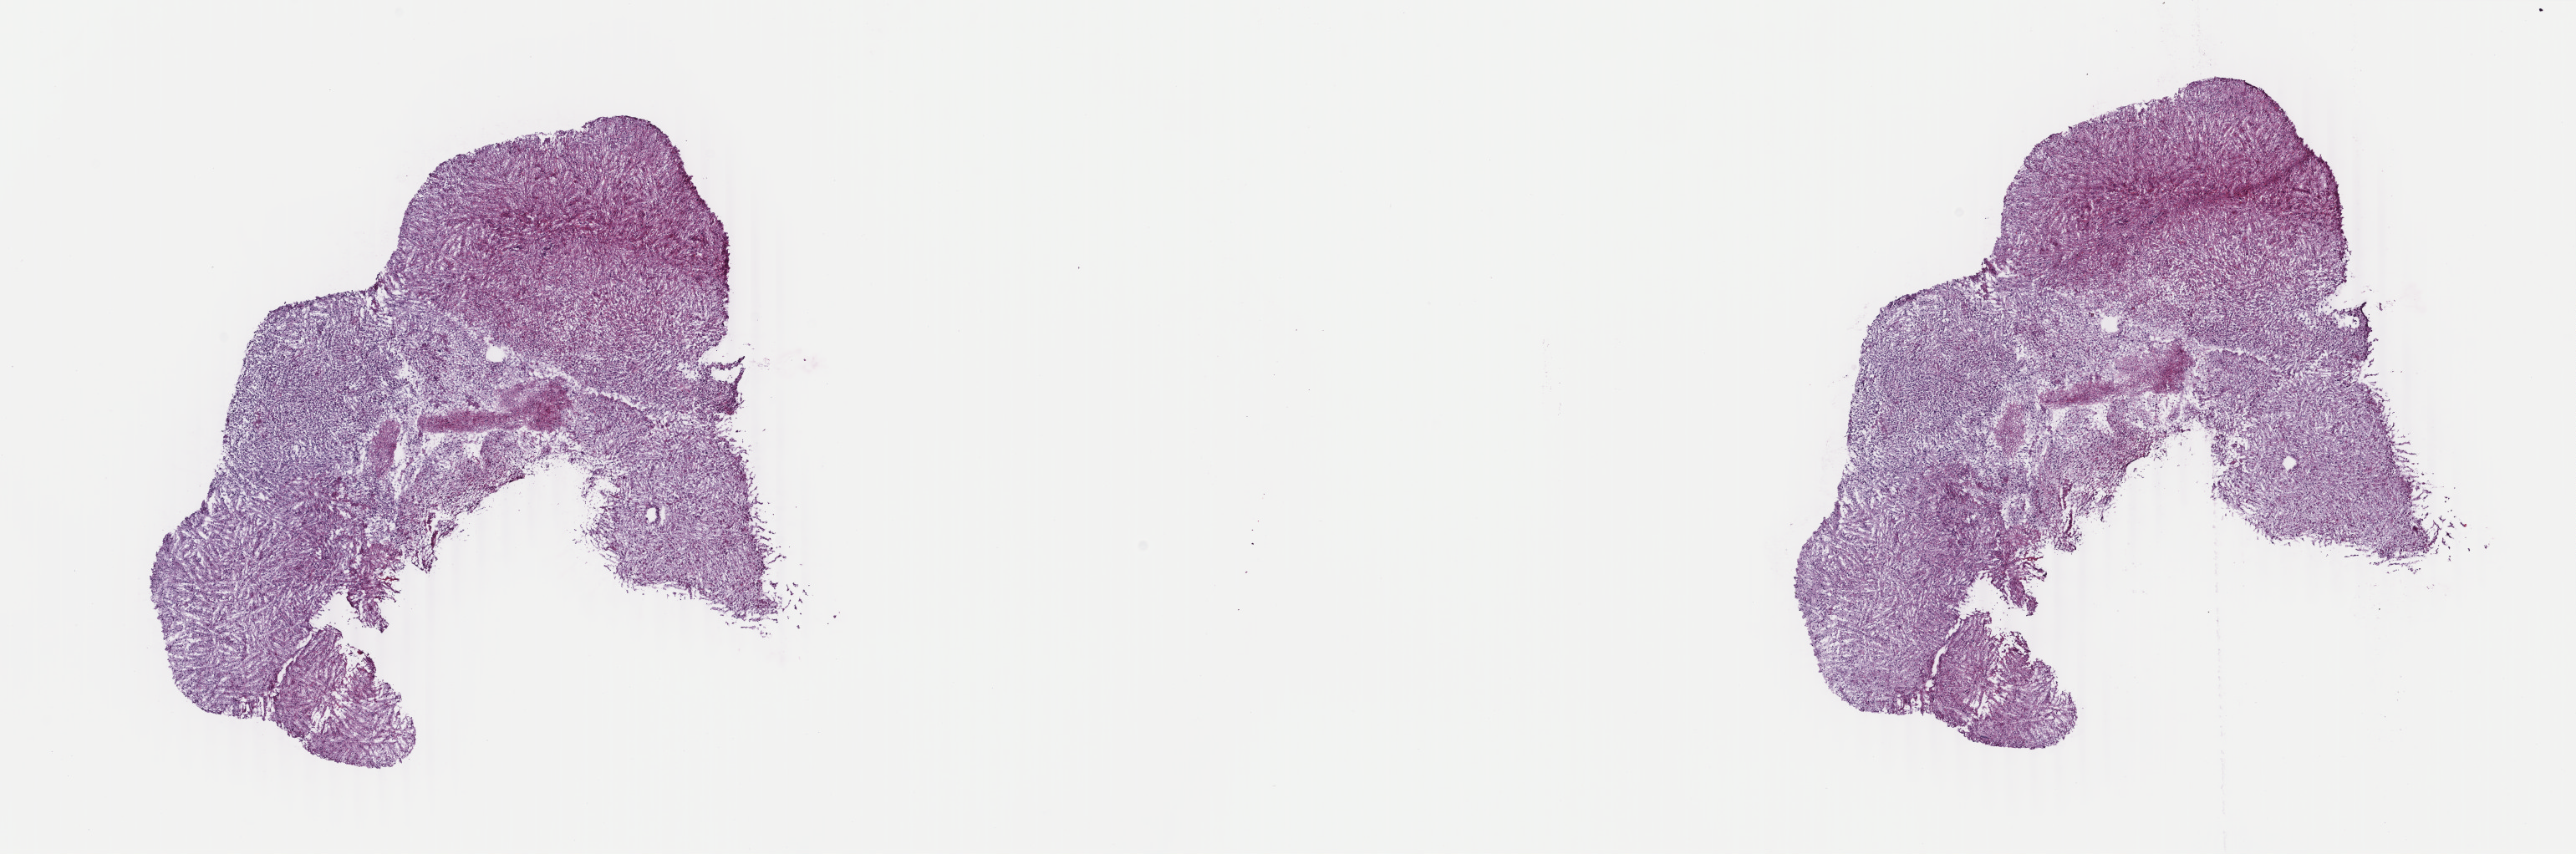
H&E-stained whole-slide image — a low-resolution overview of the entire scanned area, about 24.5 x 8.1 mm; frozen section from the top of the tissue portion; brain, primary tumour sample. Male, age 40 years at initial diagnosis. Histologic grade: G3 (poorly differentiated). Pathologist review of this section (percent, as recorded): tumour cells 60%, tumour nuclei 90%, normal cells 5%, stromal cells 35%, necrosis 0%. Infiltration values recorded for this section: lymphocyte infiltration 0%, monocyte infiltration 0%, neutrophil infiltration 0%.
Laterality: right. Histologic diagnosis: Astrocytoma, anaplastic.